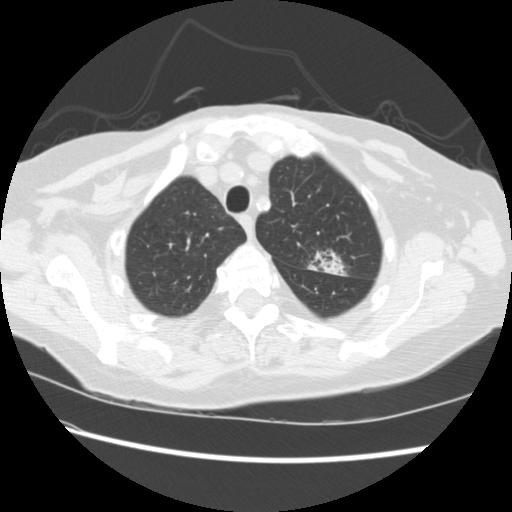
Chest CT (low-dose screening protocol), one axial image; baseline screening round; lung window (W 1500 / L -600 HU); 512 × 512 image matrix, field of view 340 × 340 mm. Female, age 74 years at enrolment.
Expert reader's lesion annotation, bounding box [x1, y1, x2, y2] px = [297, 243, 347, 283]. The screening reader recorded 2 non-calcified nodules or masses ≥4 mm on this exam (left upper lobe, right lower lobe); which of them this box marks is not recorded.